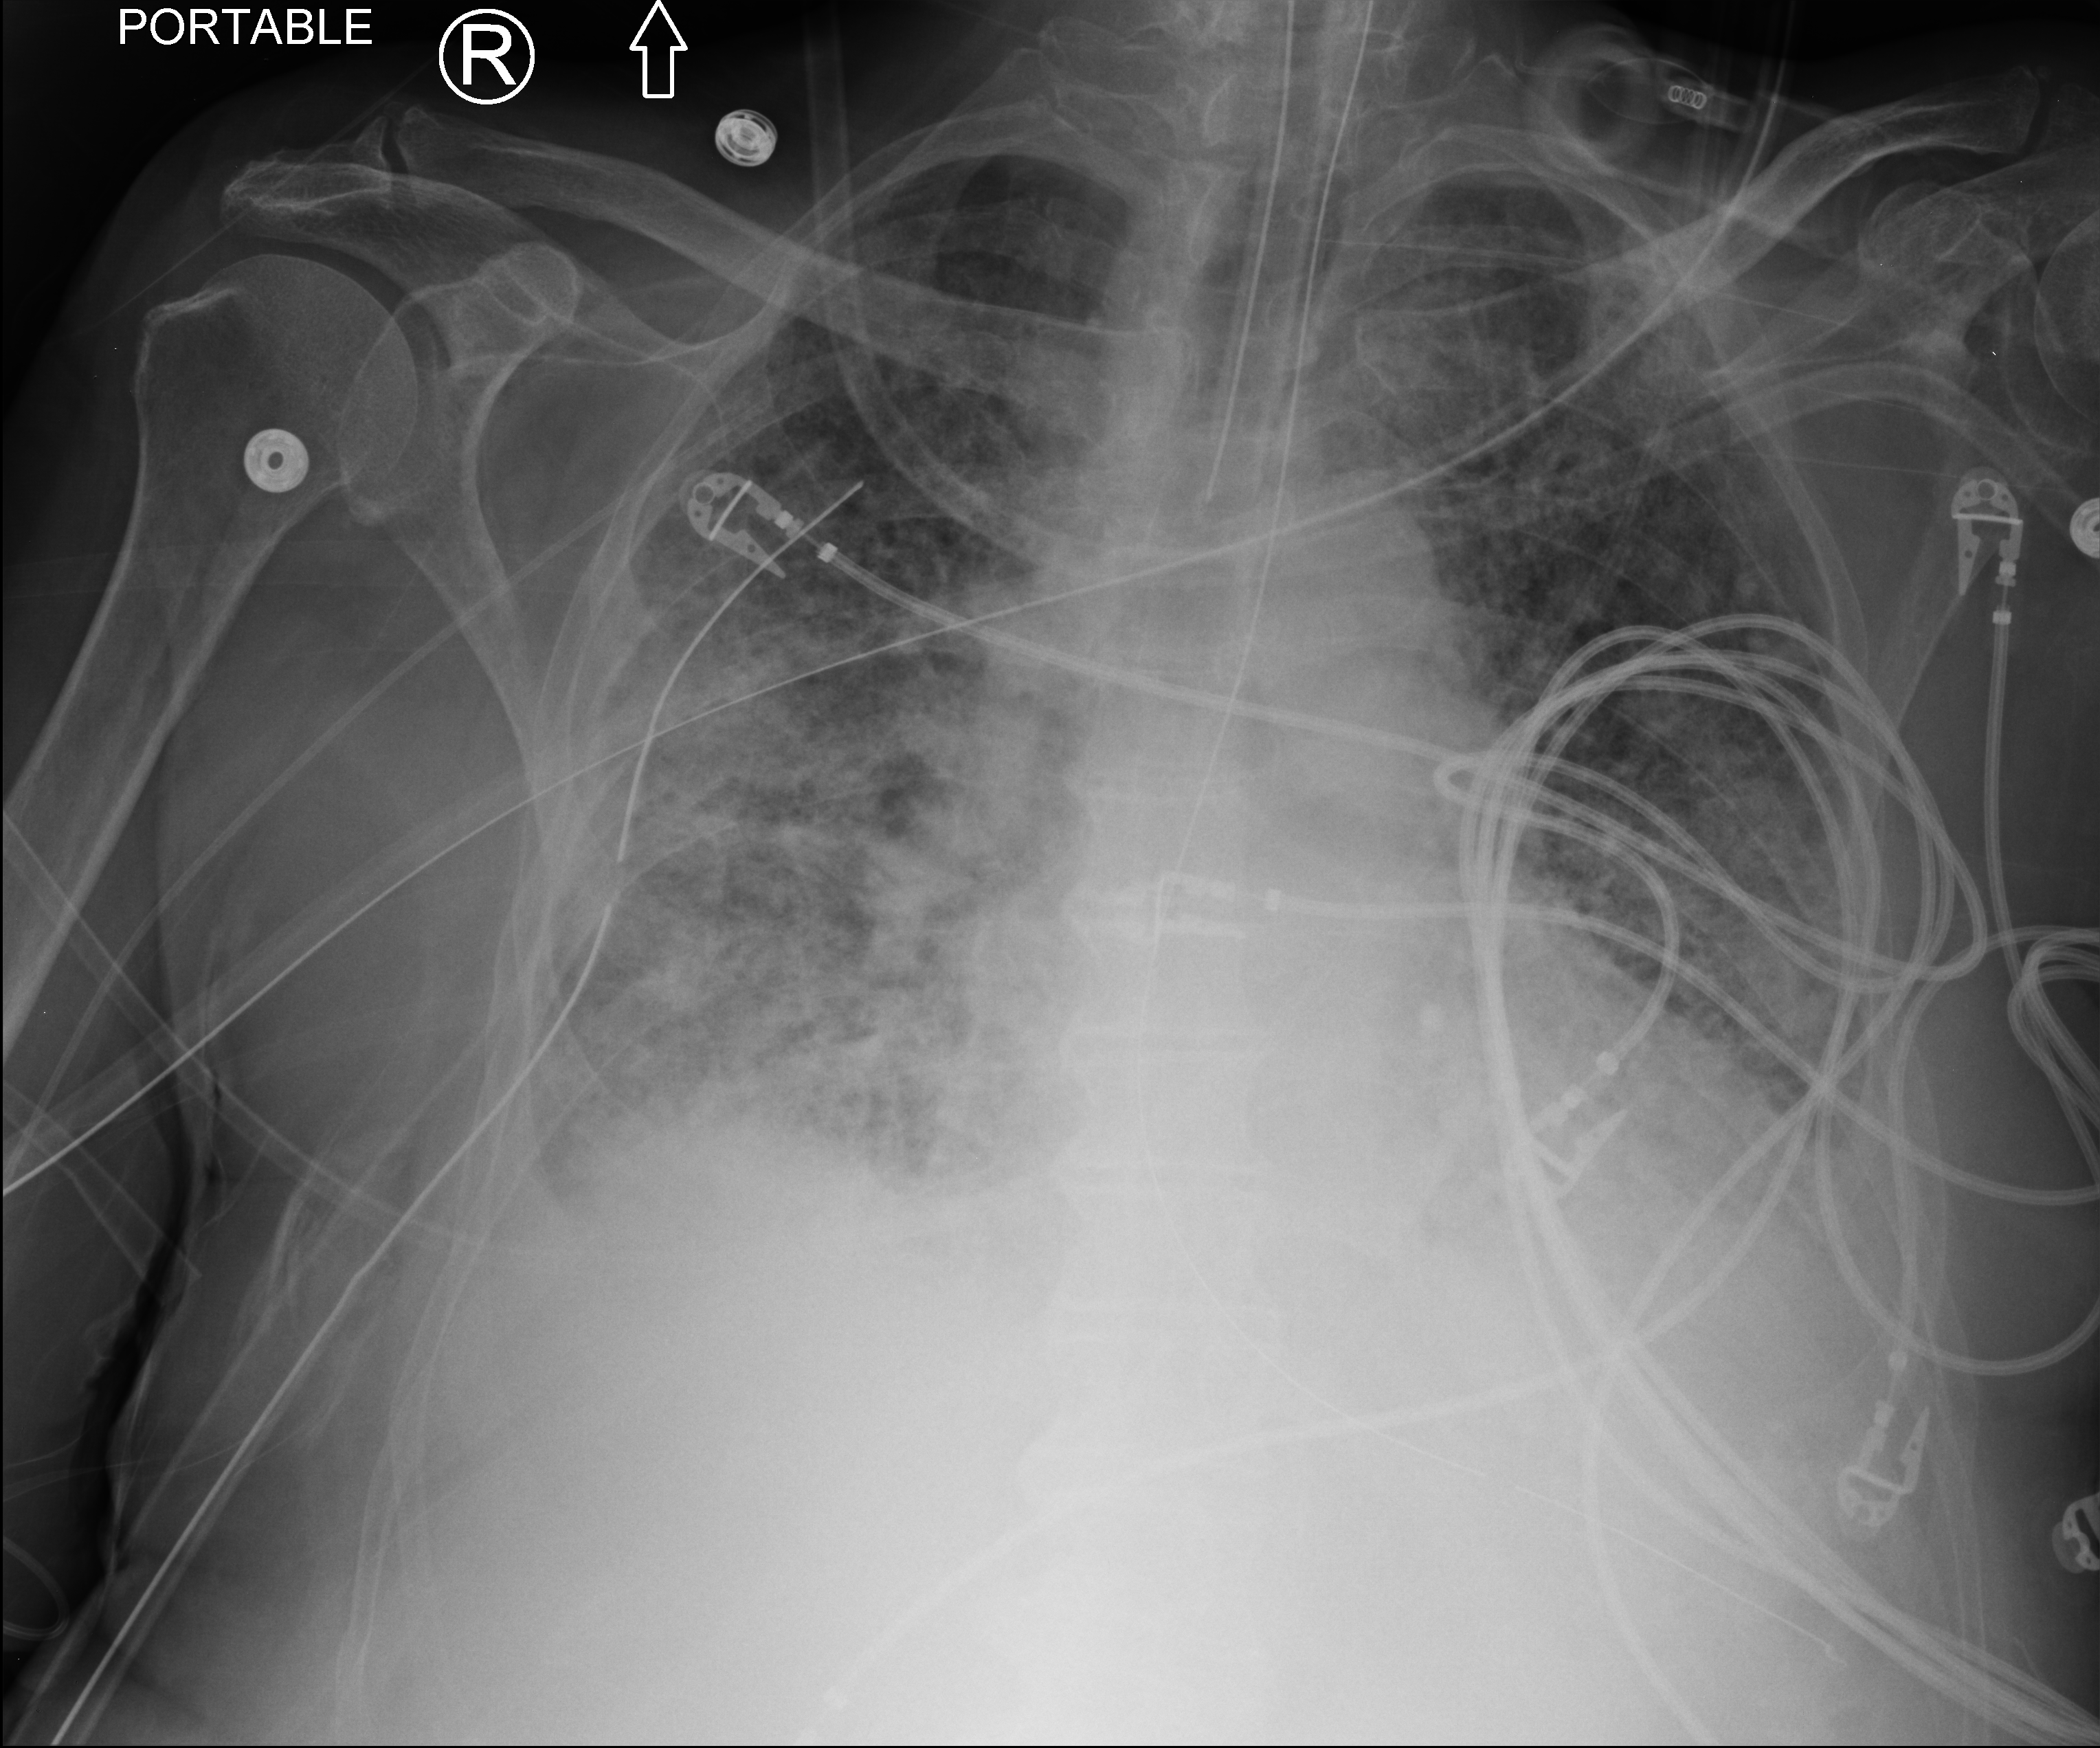
Chest X-ray (portable), anteroposterior (AP) projection. Male patient hospitalised with COVID-19, age 75–90 years.
Hospital-stay facts (about this admission, not read from this image; timing relative to this image not recorded): admitted to intensive care during this hospital stay: yes; mechanically ventilated during this hospital stay: yes.